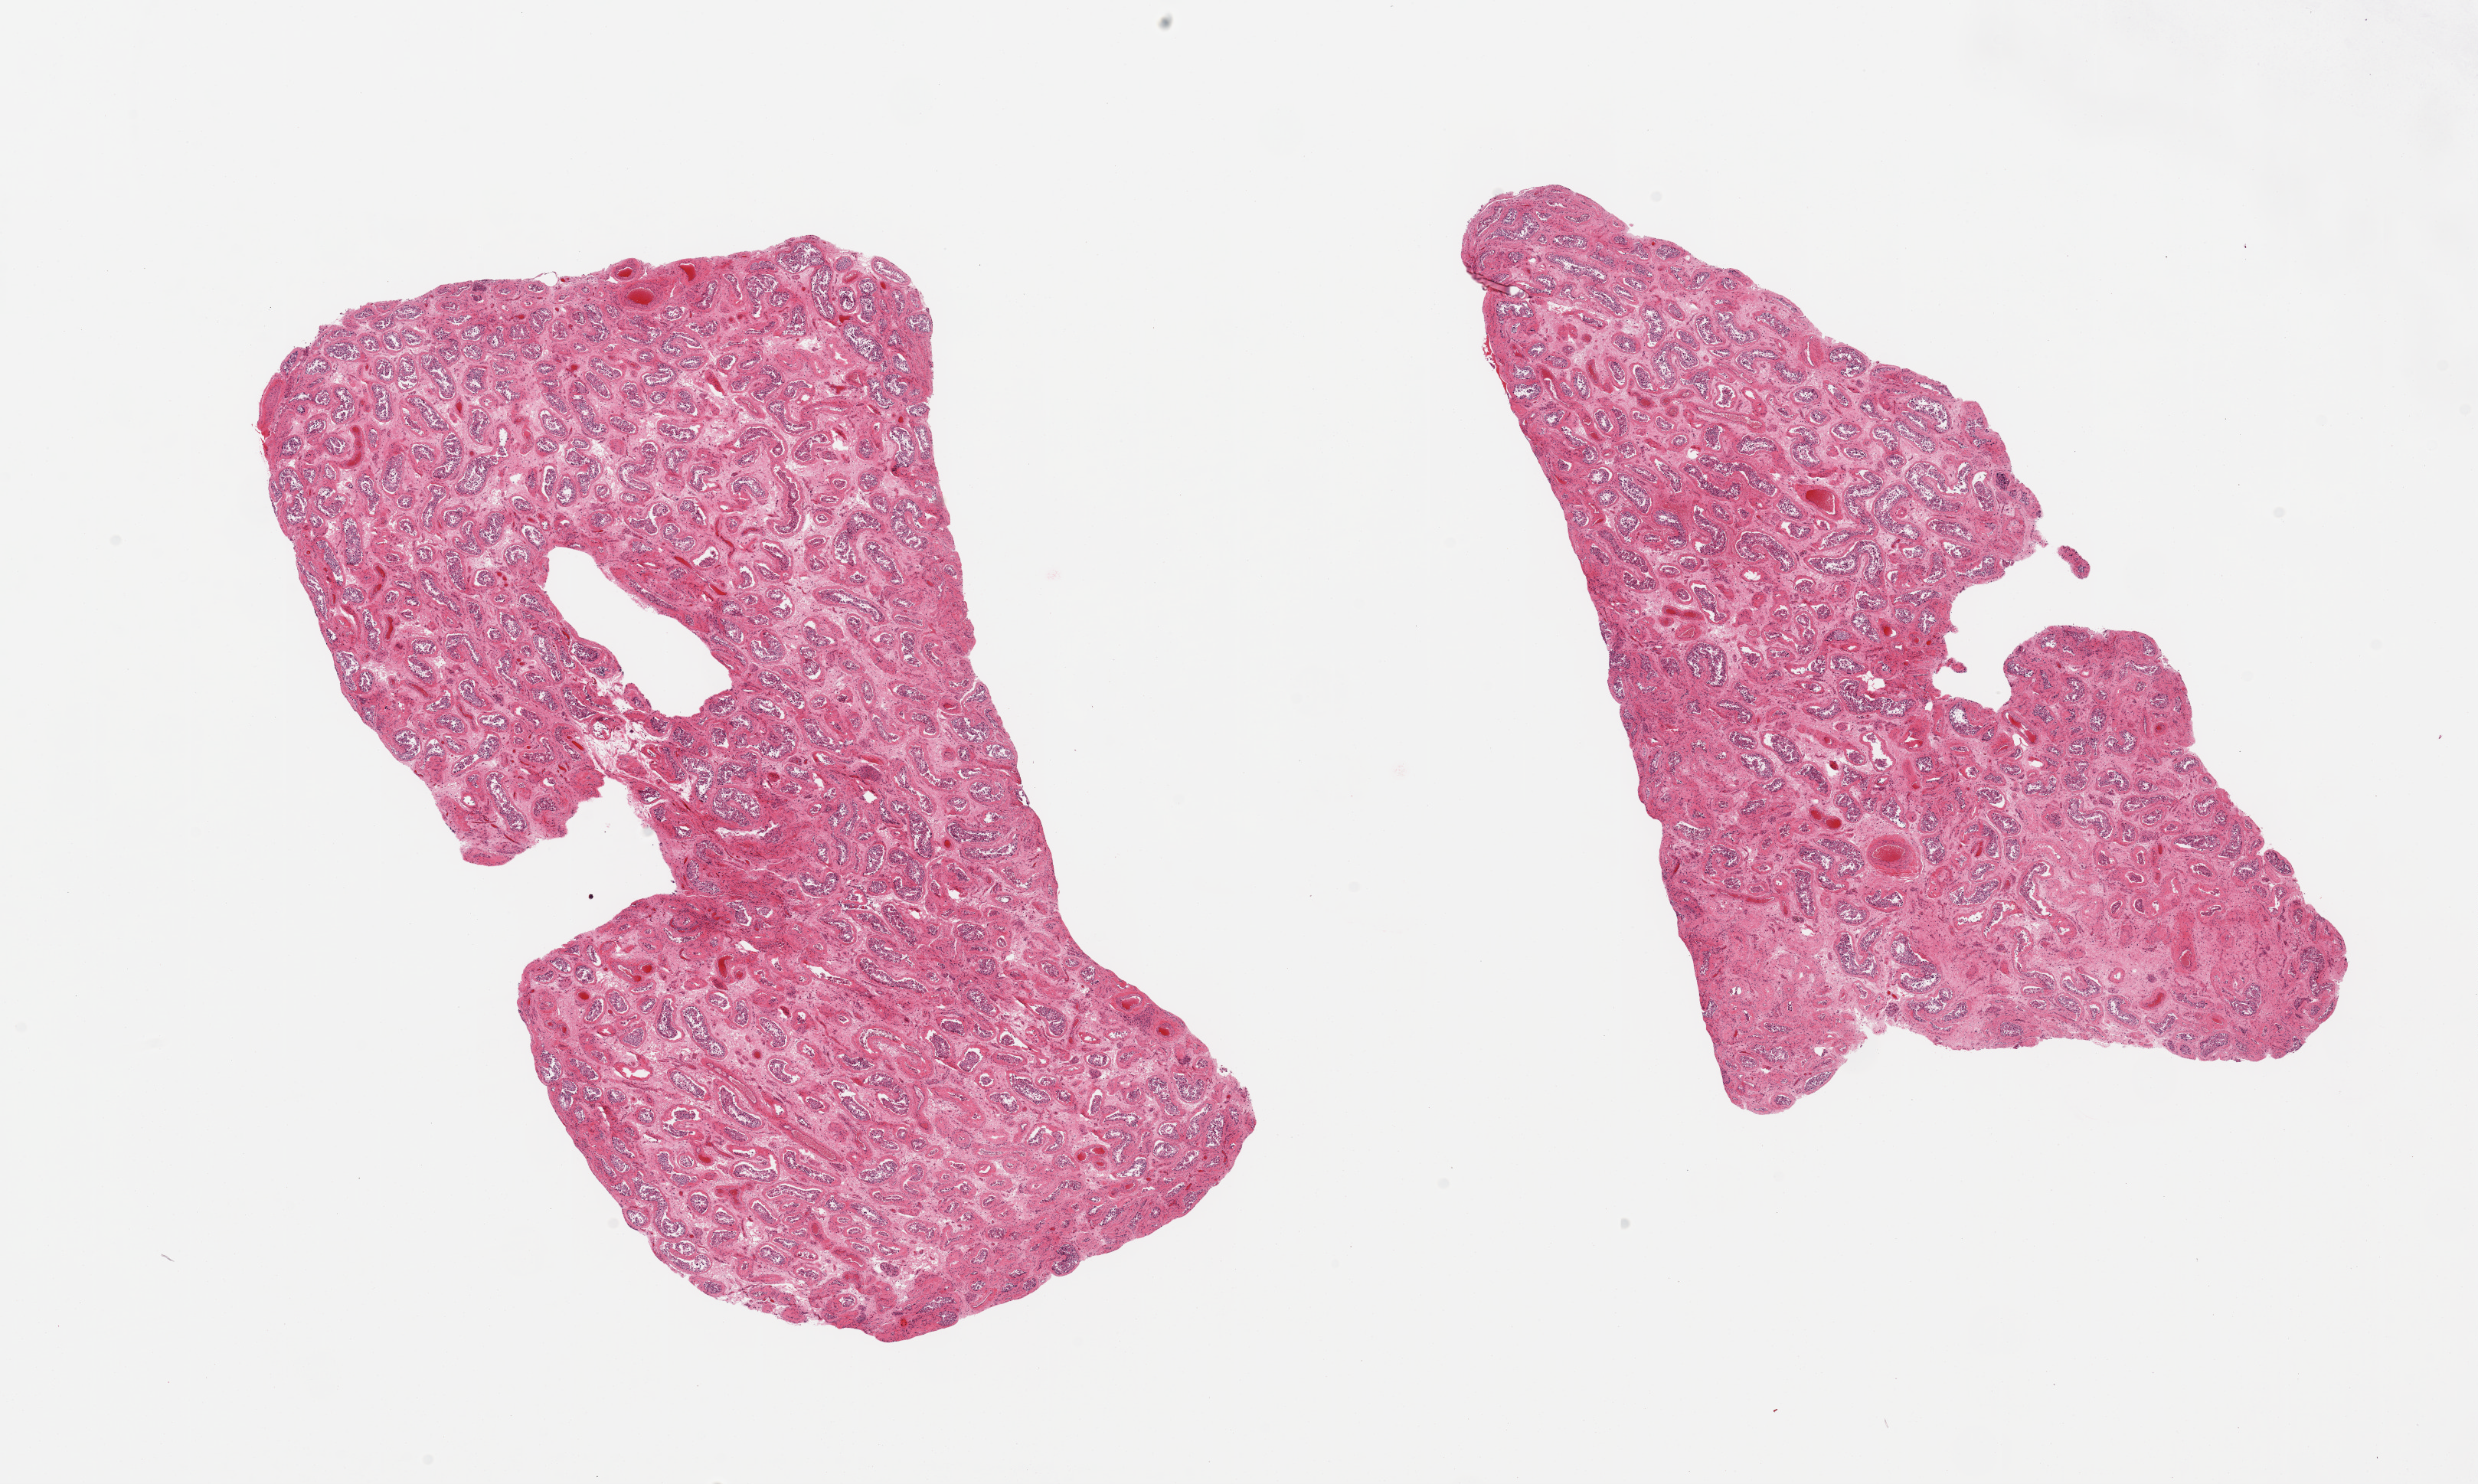
H&E whole-slide image — a low-resolution overview of the entire scanned area, about 25.6 x 15.3 mm. PAXgene-fixed, paraffin-embedded tissue. Section of testis (target tissue). Donor tissue sample. Donor: male.
* review note (as recorded): 2 pieces; peritubular and interstitial fibrosis